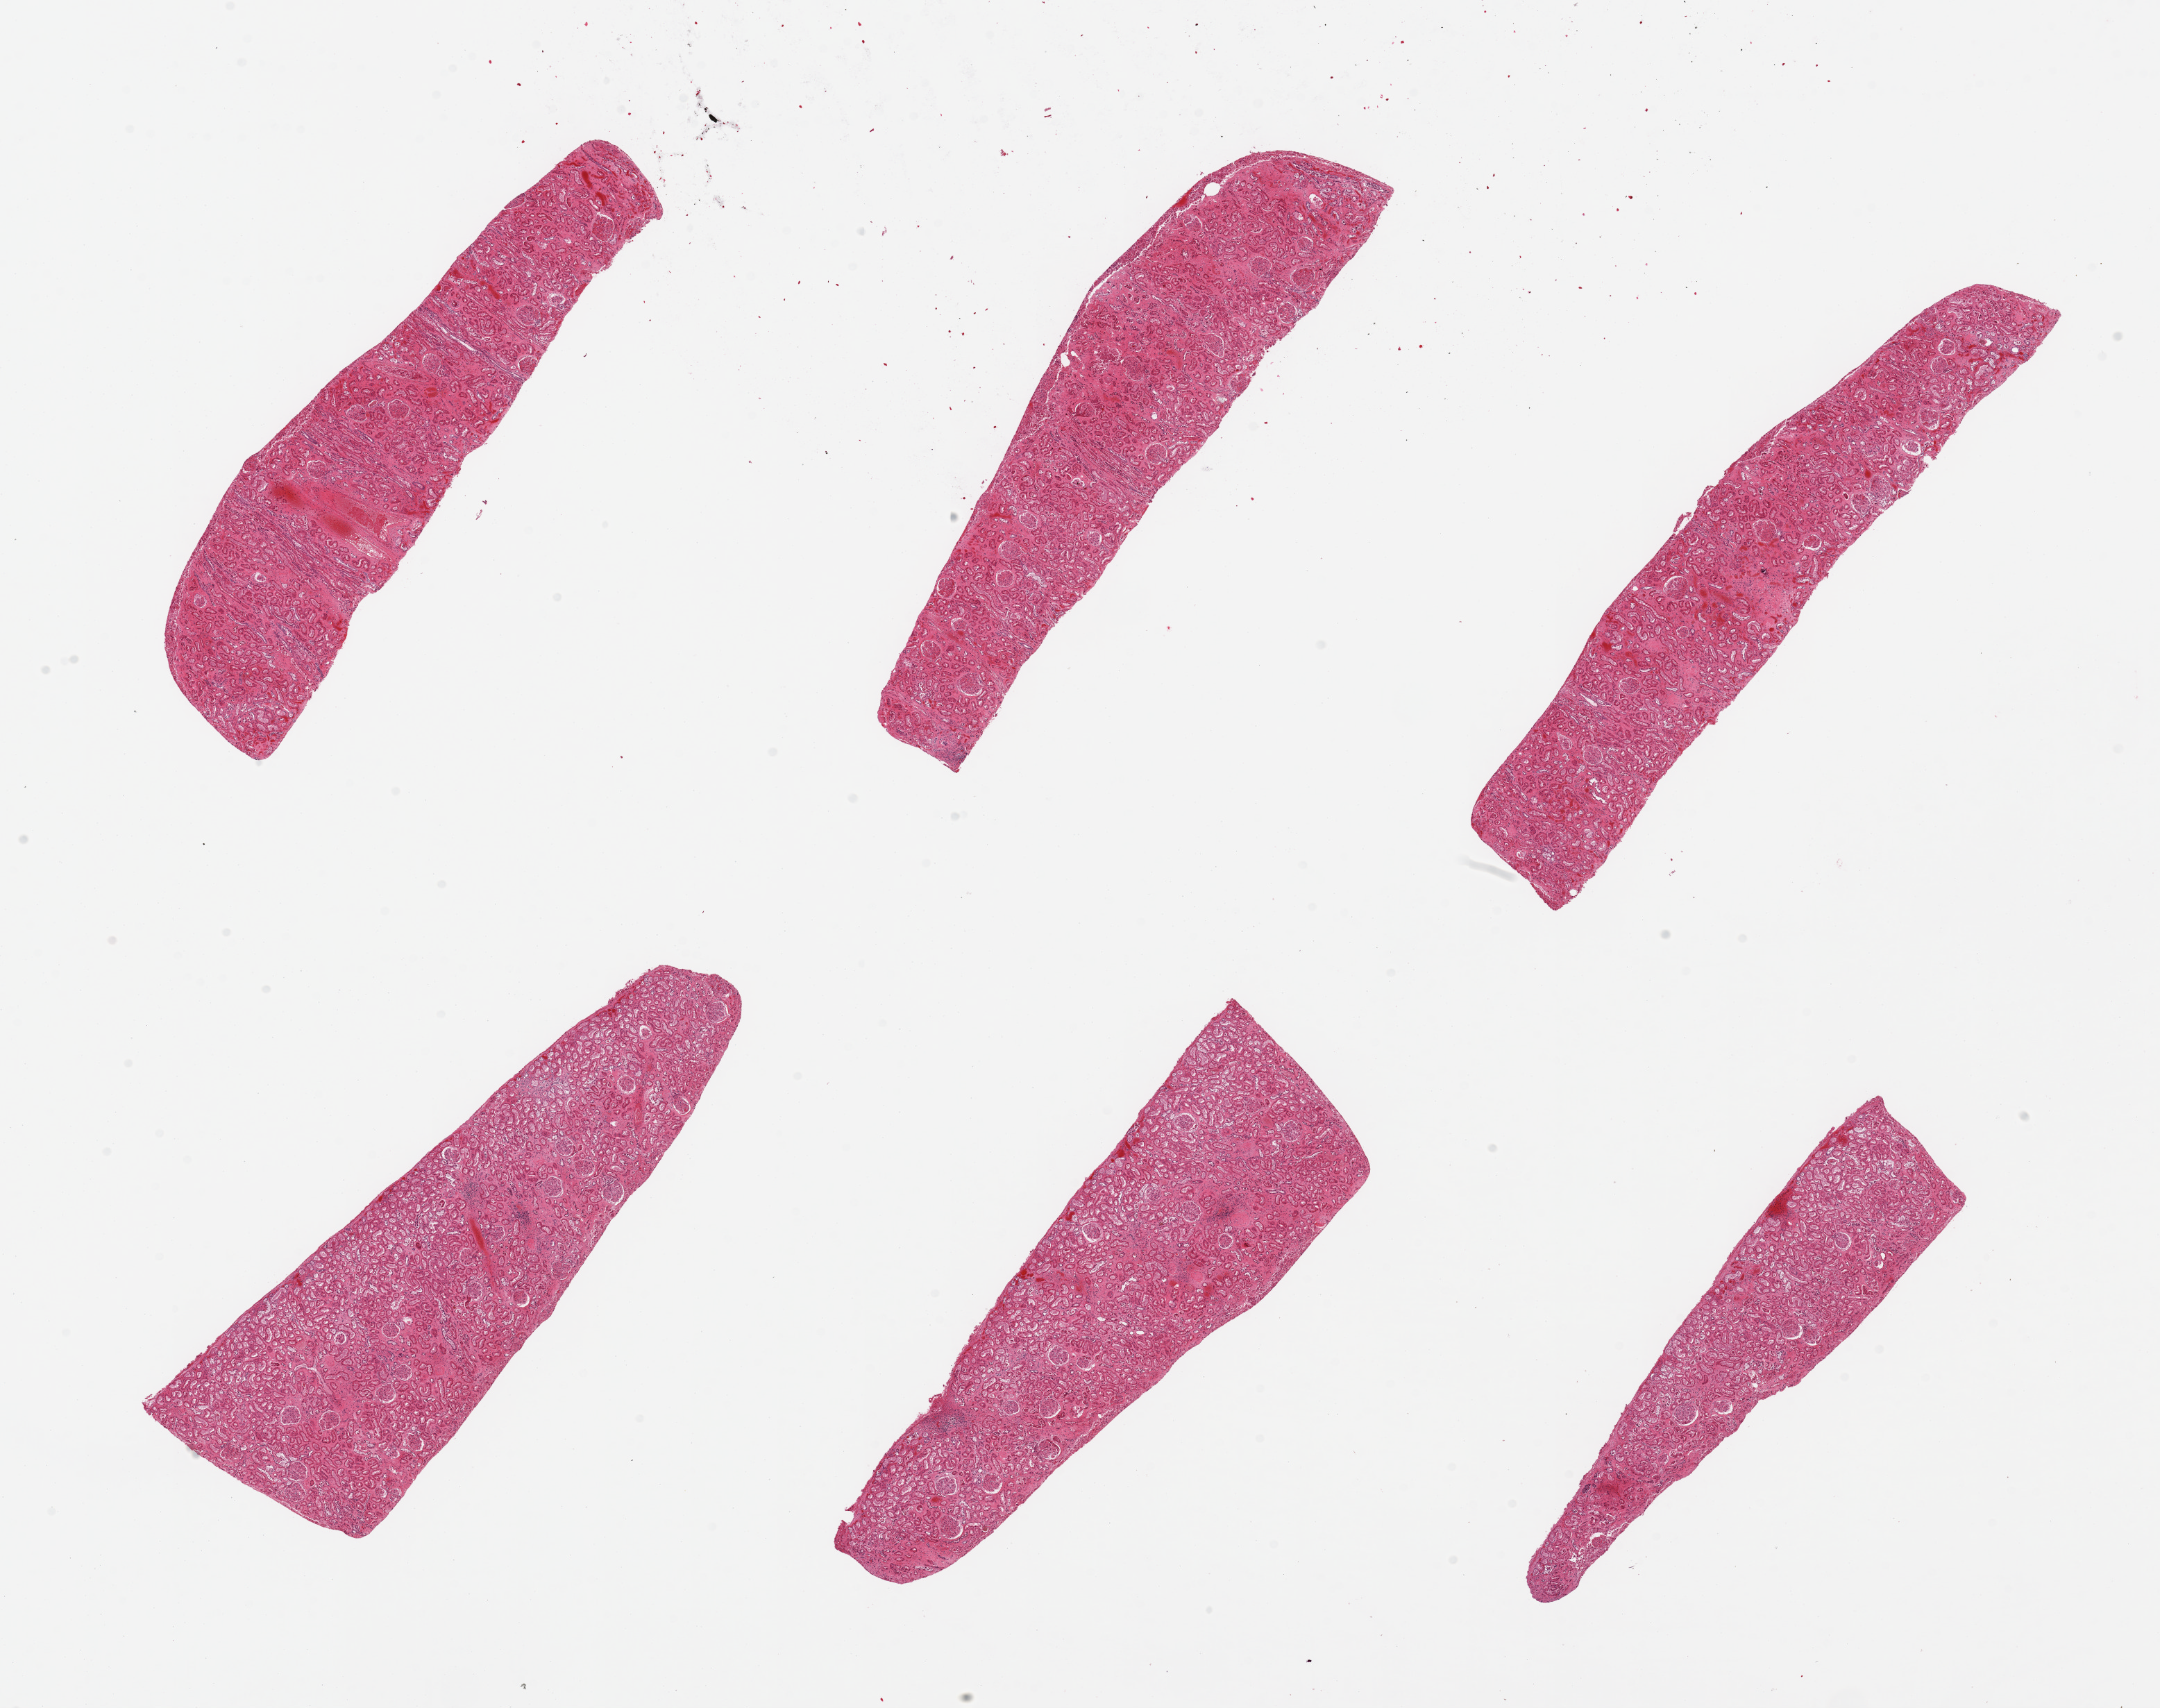
Whole-slide image, H&E stain, a low-resolution overview of the entire scanned area, about 24.6 x 19.5 mm, PAXgene-fixed, paraffin-embedded tissue, target tissue: renal cortex, donor tissue sample. Male donor.
- reviewer comment on this tissue sample: 6 pieces; glomeruli in all sections, occasional sclerotic glomeruli